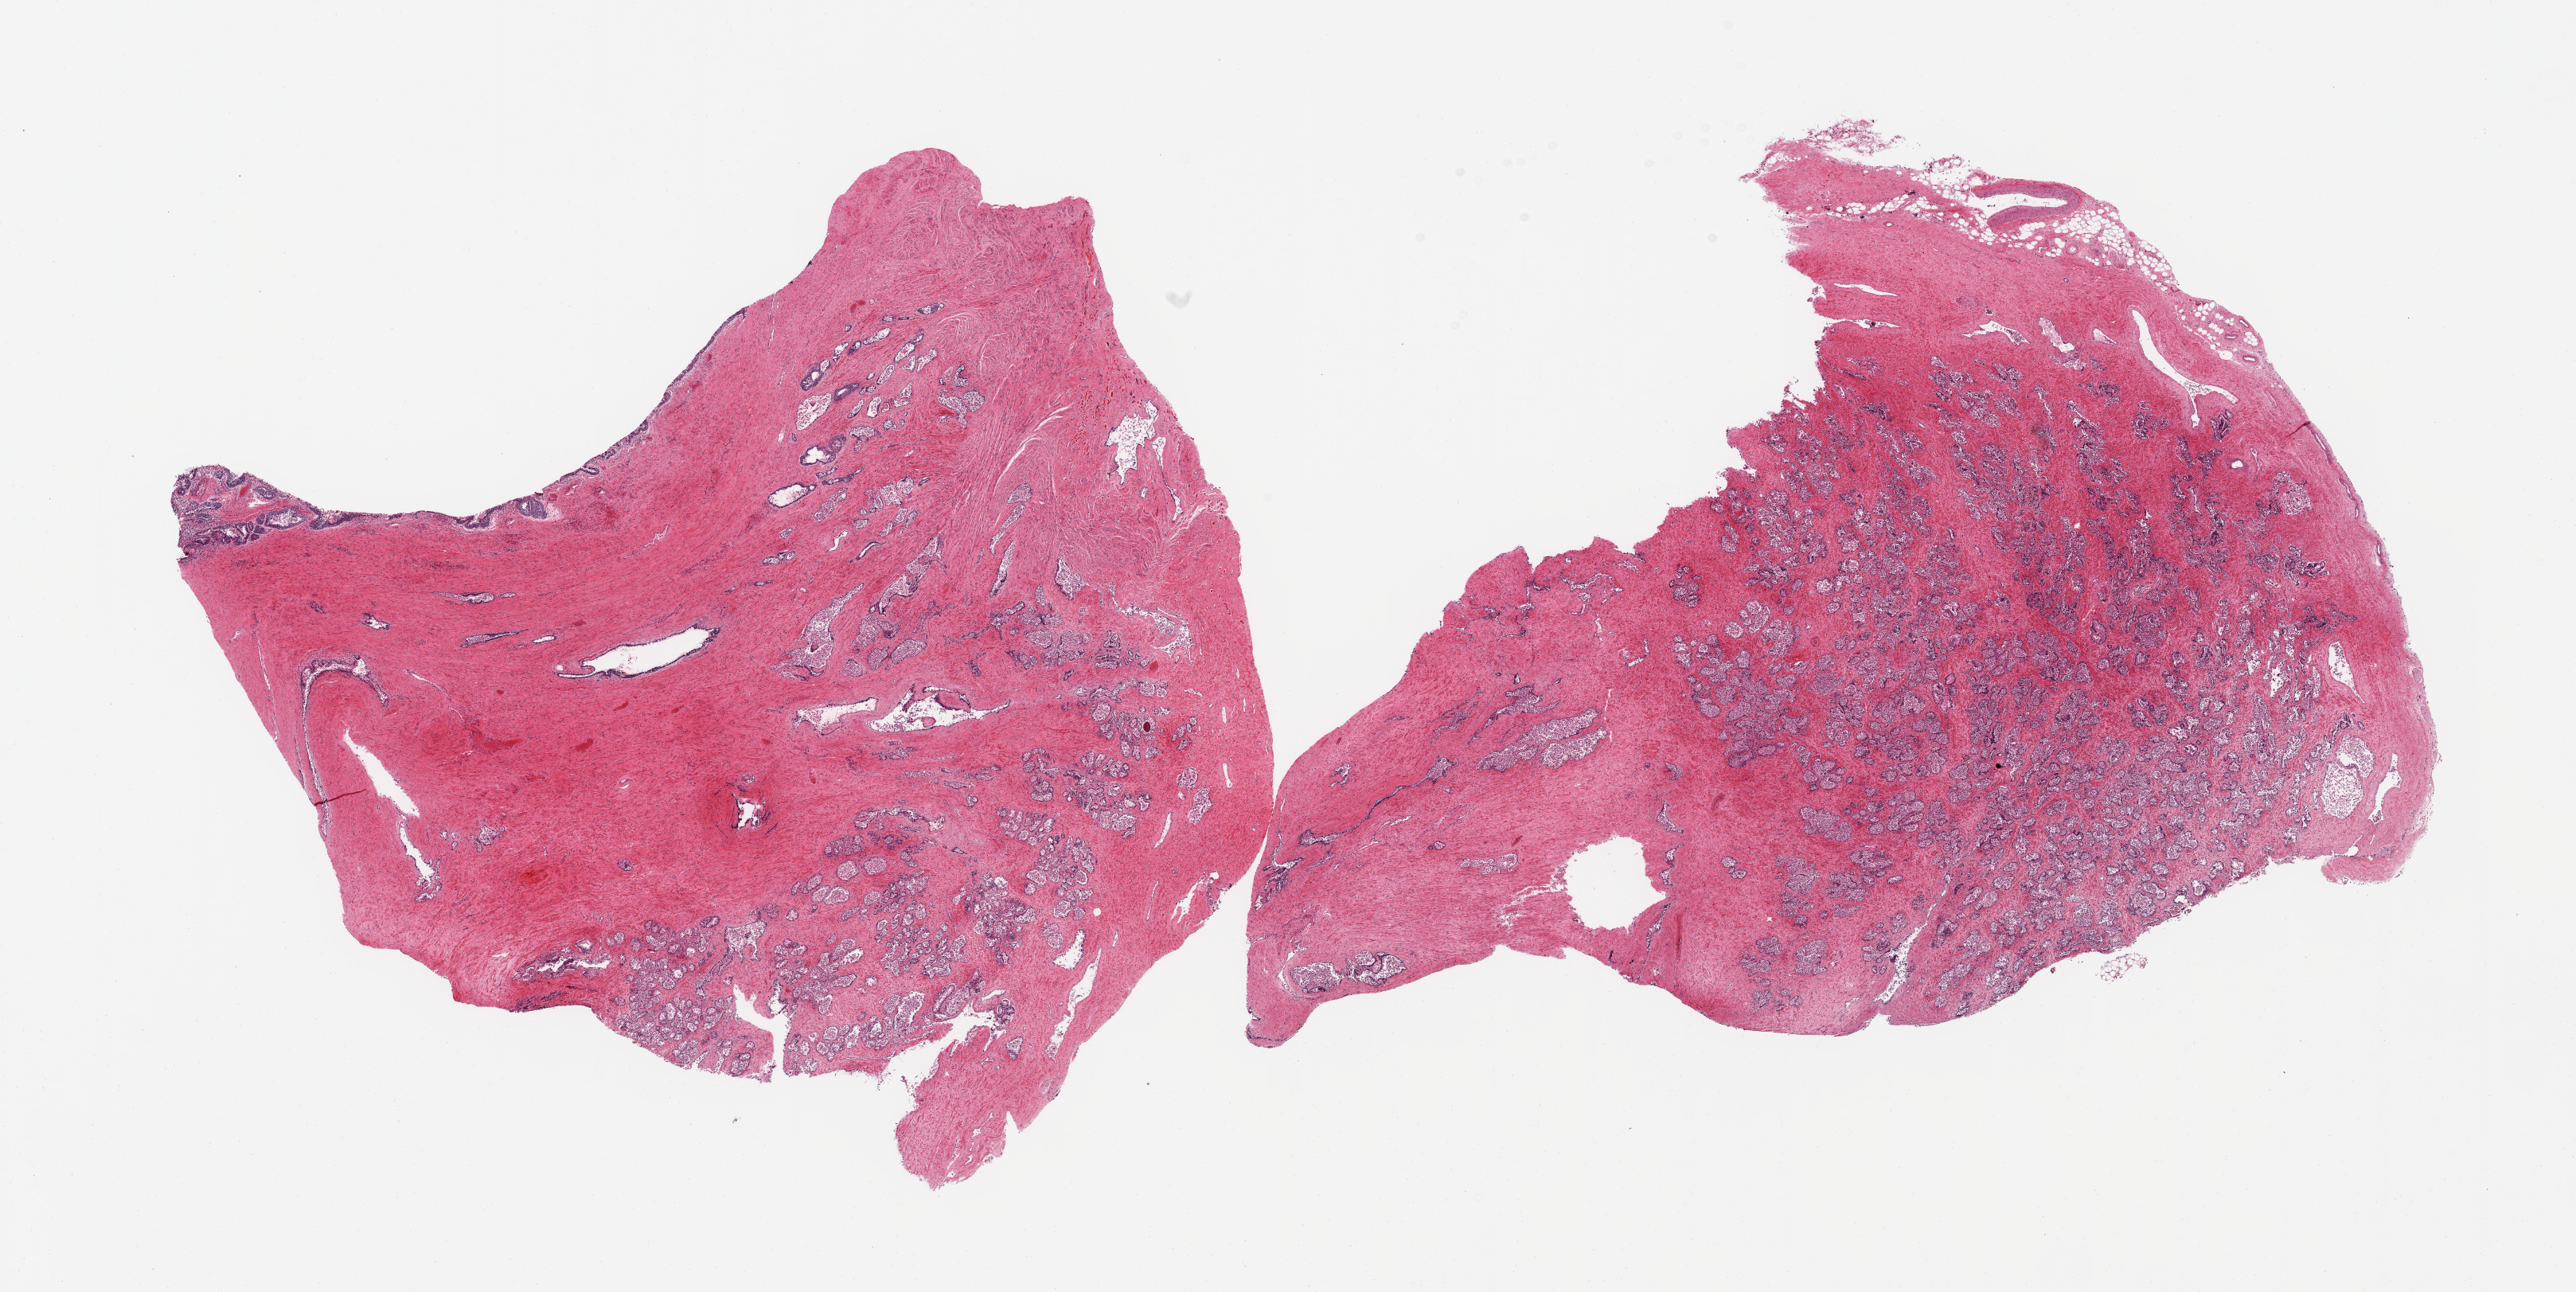
Whole-slide image, H&E stain — low-resolution overview of the scanned area, about 25.6 x 12.8 mm (acquisition: 20x scan); PAXgene-fixed paraffin-embedded (PFPE) section; target tissue: prostate; tissue donor sample. Donor sex: male.
Pathologist's review note for this sample: 2 pieces, glandular elements with advanced autolysis.